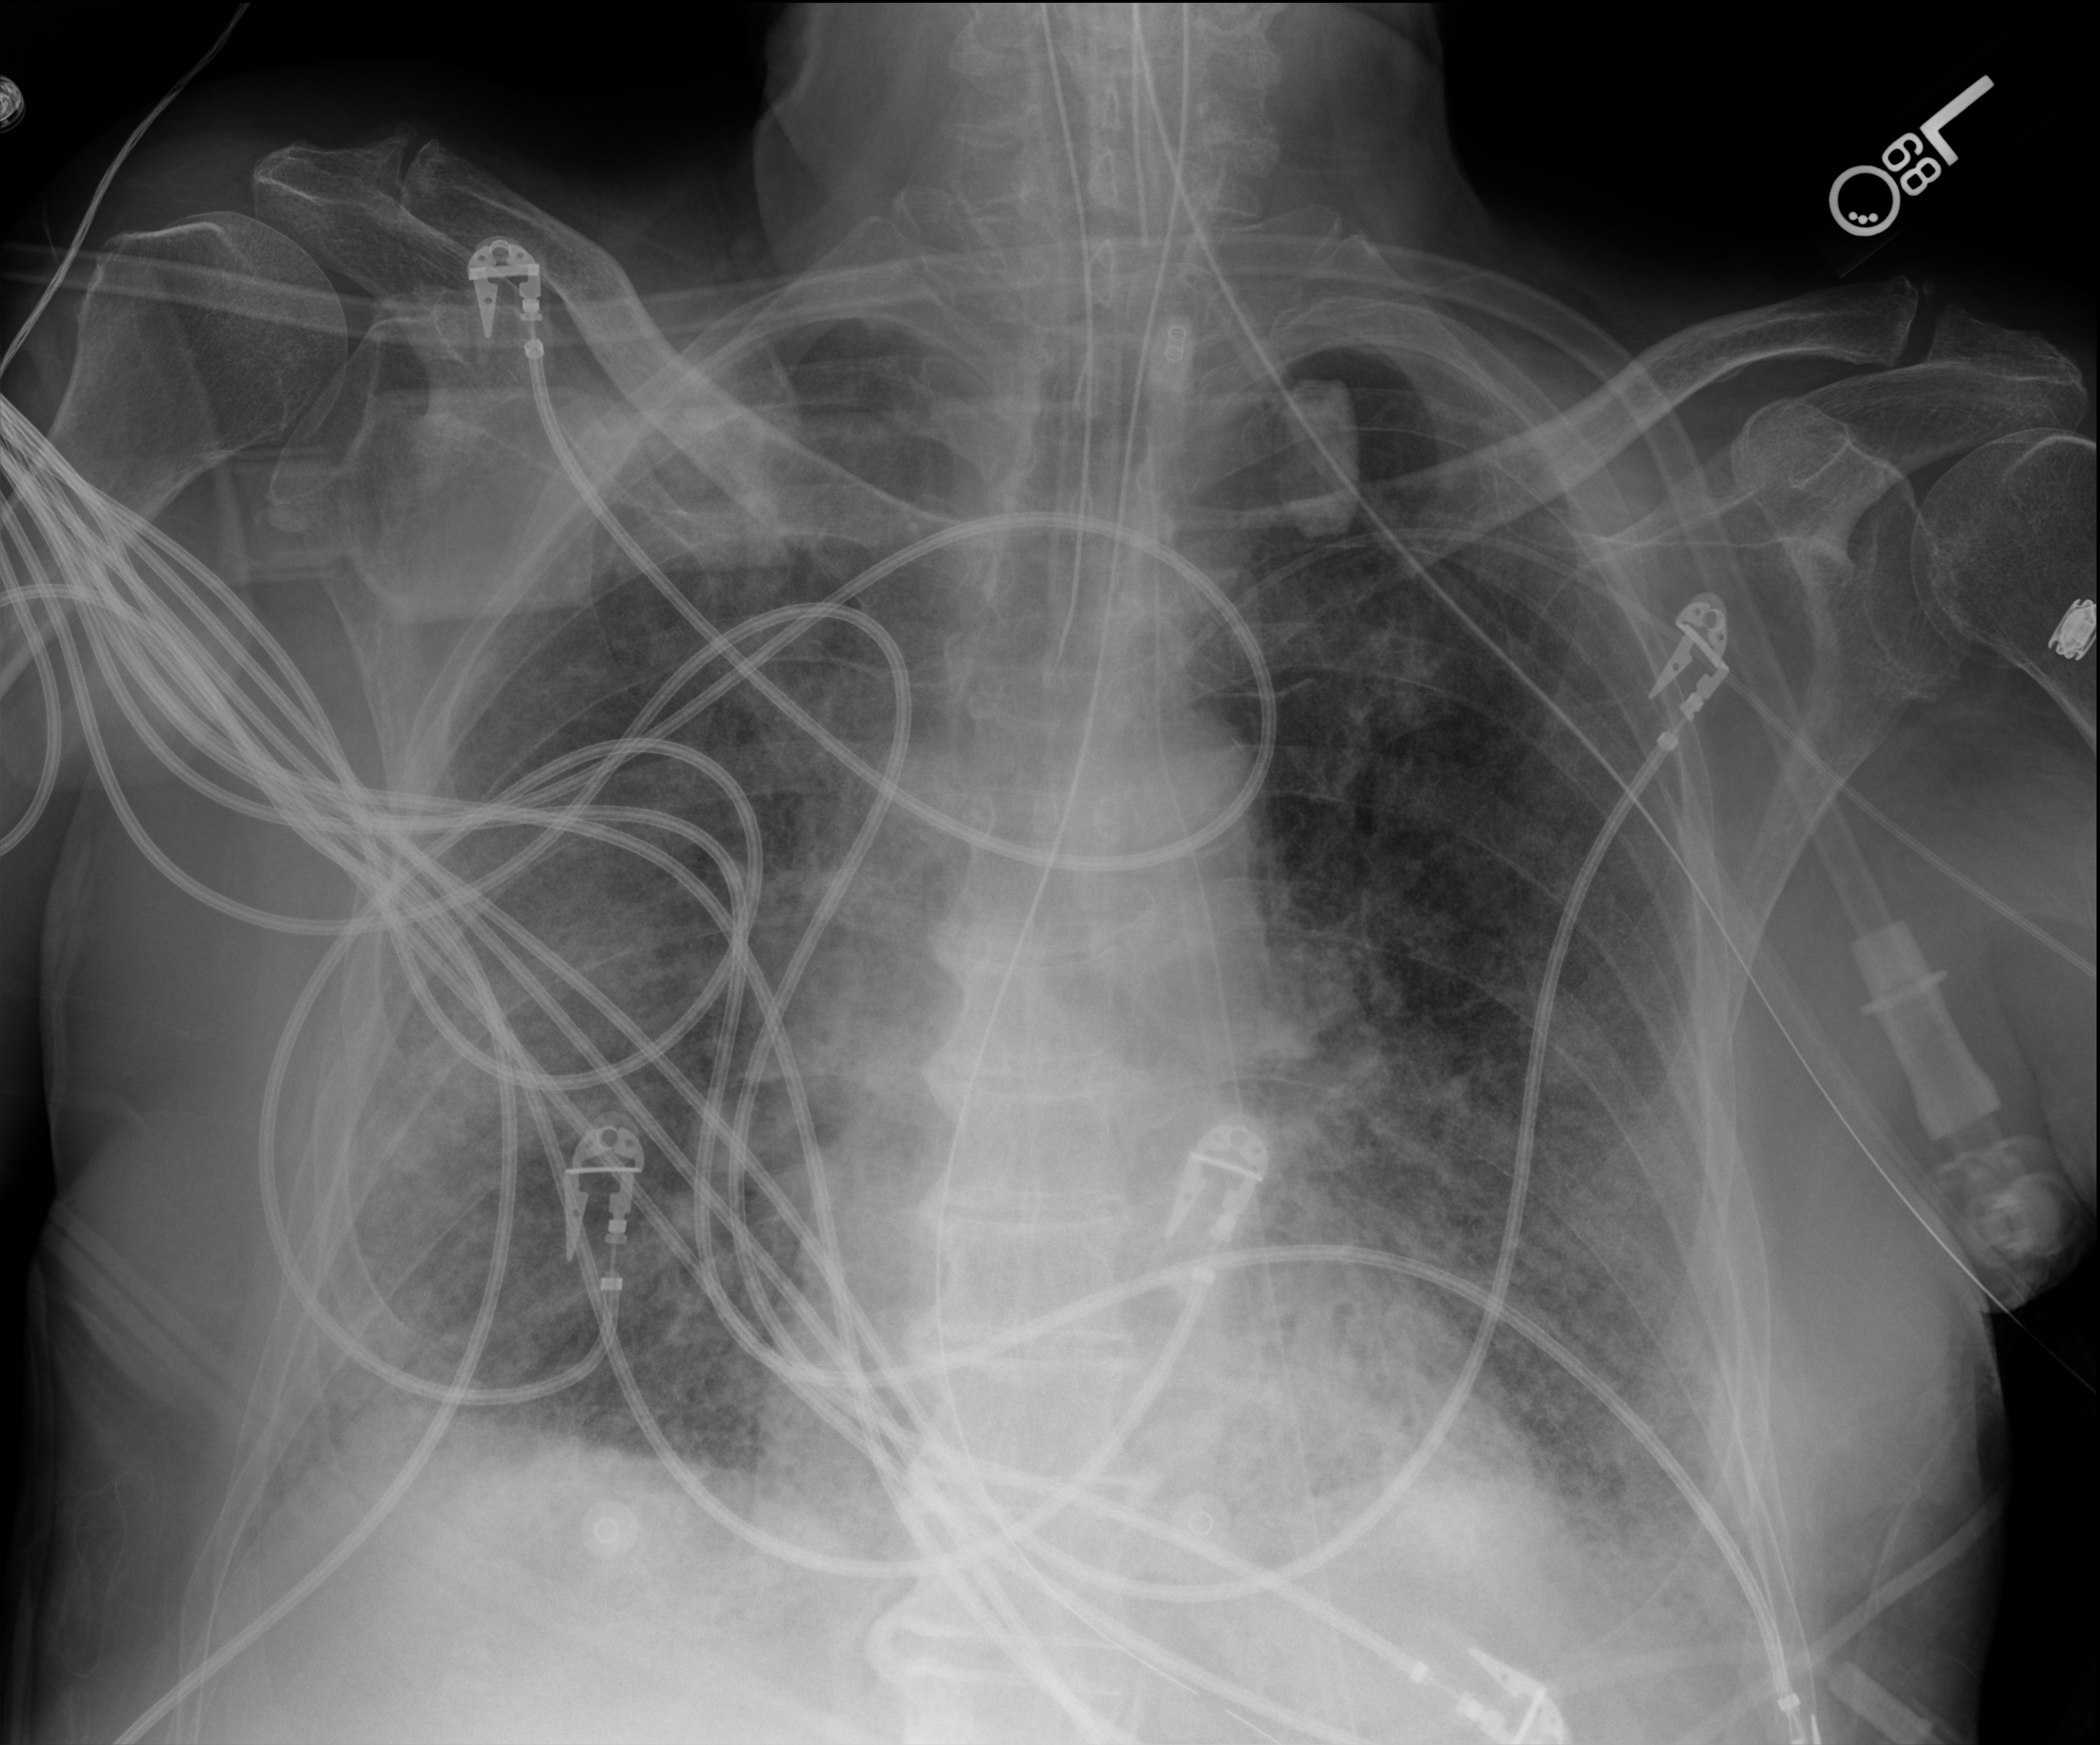
Bedside chest radiograph (digital radiography), anteroposterior (AP) projection. Male patient hospitalised with COVID-19, age 75–90 years.
Hospital-stay facts (about this admission, not read from this image; timing relative to this image not recorded):
- admitted to intensive care during this hospital stay: yes
- COPD (admission record): no
- chronic kidney disease (admission record): no